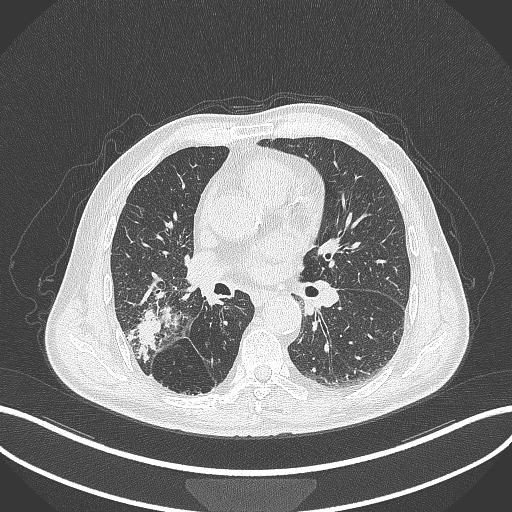
Chest CT, one axial slice; position 216 of 429 along the scan axis; reconstruction kernel B70f; 120 kVp; lung window (W 1500 / L -600 HU); 1 mm slice thickness; 512 × 512 image matrix, field of view 400 × 400 mm. Male patient, age 72 years. Case-level facts recorded for this patient, not image findings: clinical TNM (as recorded): T3 N2 M0.
Outlined on this slice (rectangle marked by the reading radiologist):
- lung tumour (recorded histology: adenocarcinoma): bounding box (x1, y1, x2, y2) in pixels: (128, 305, 164, 359)